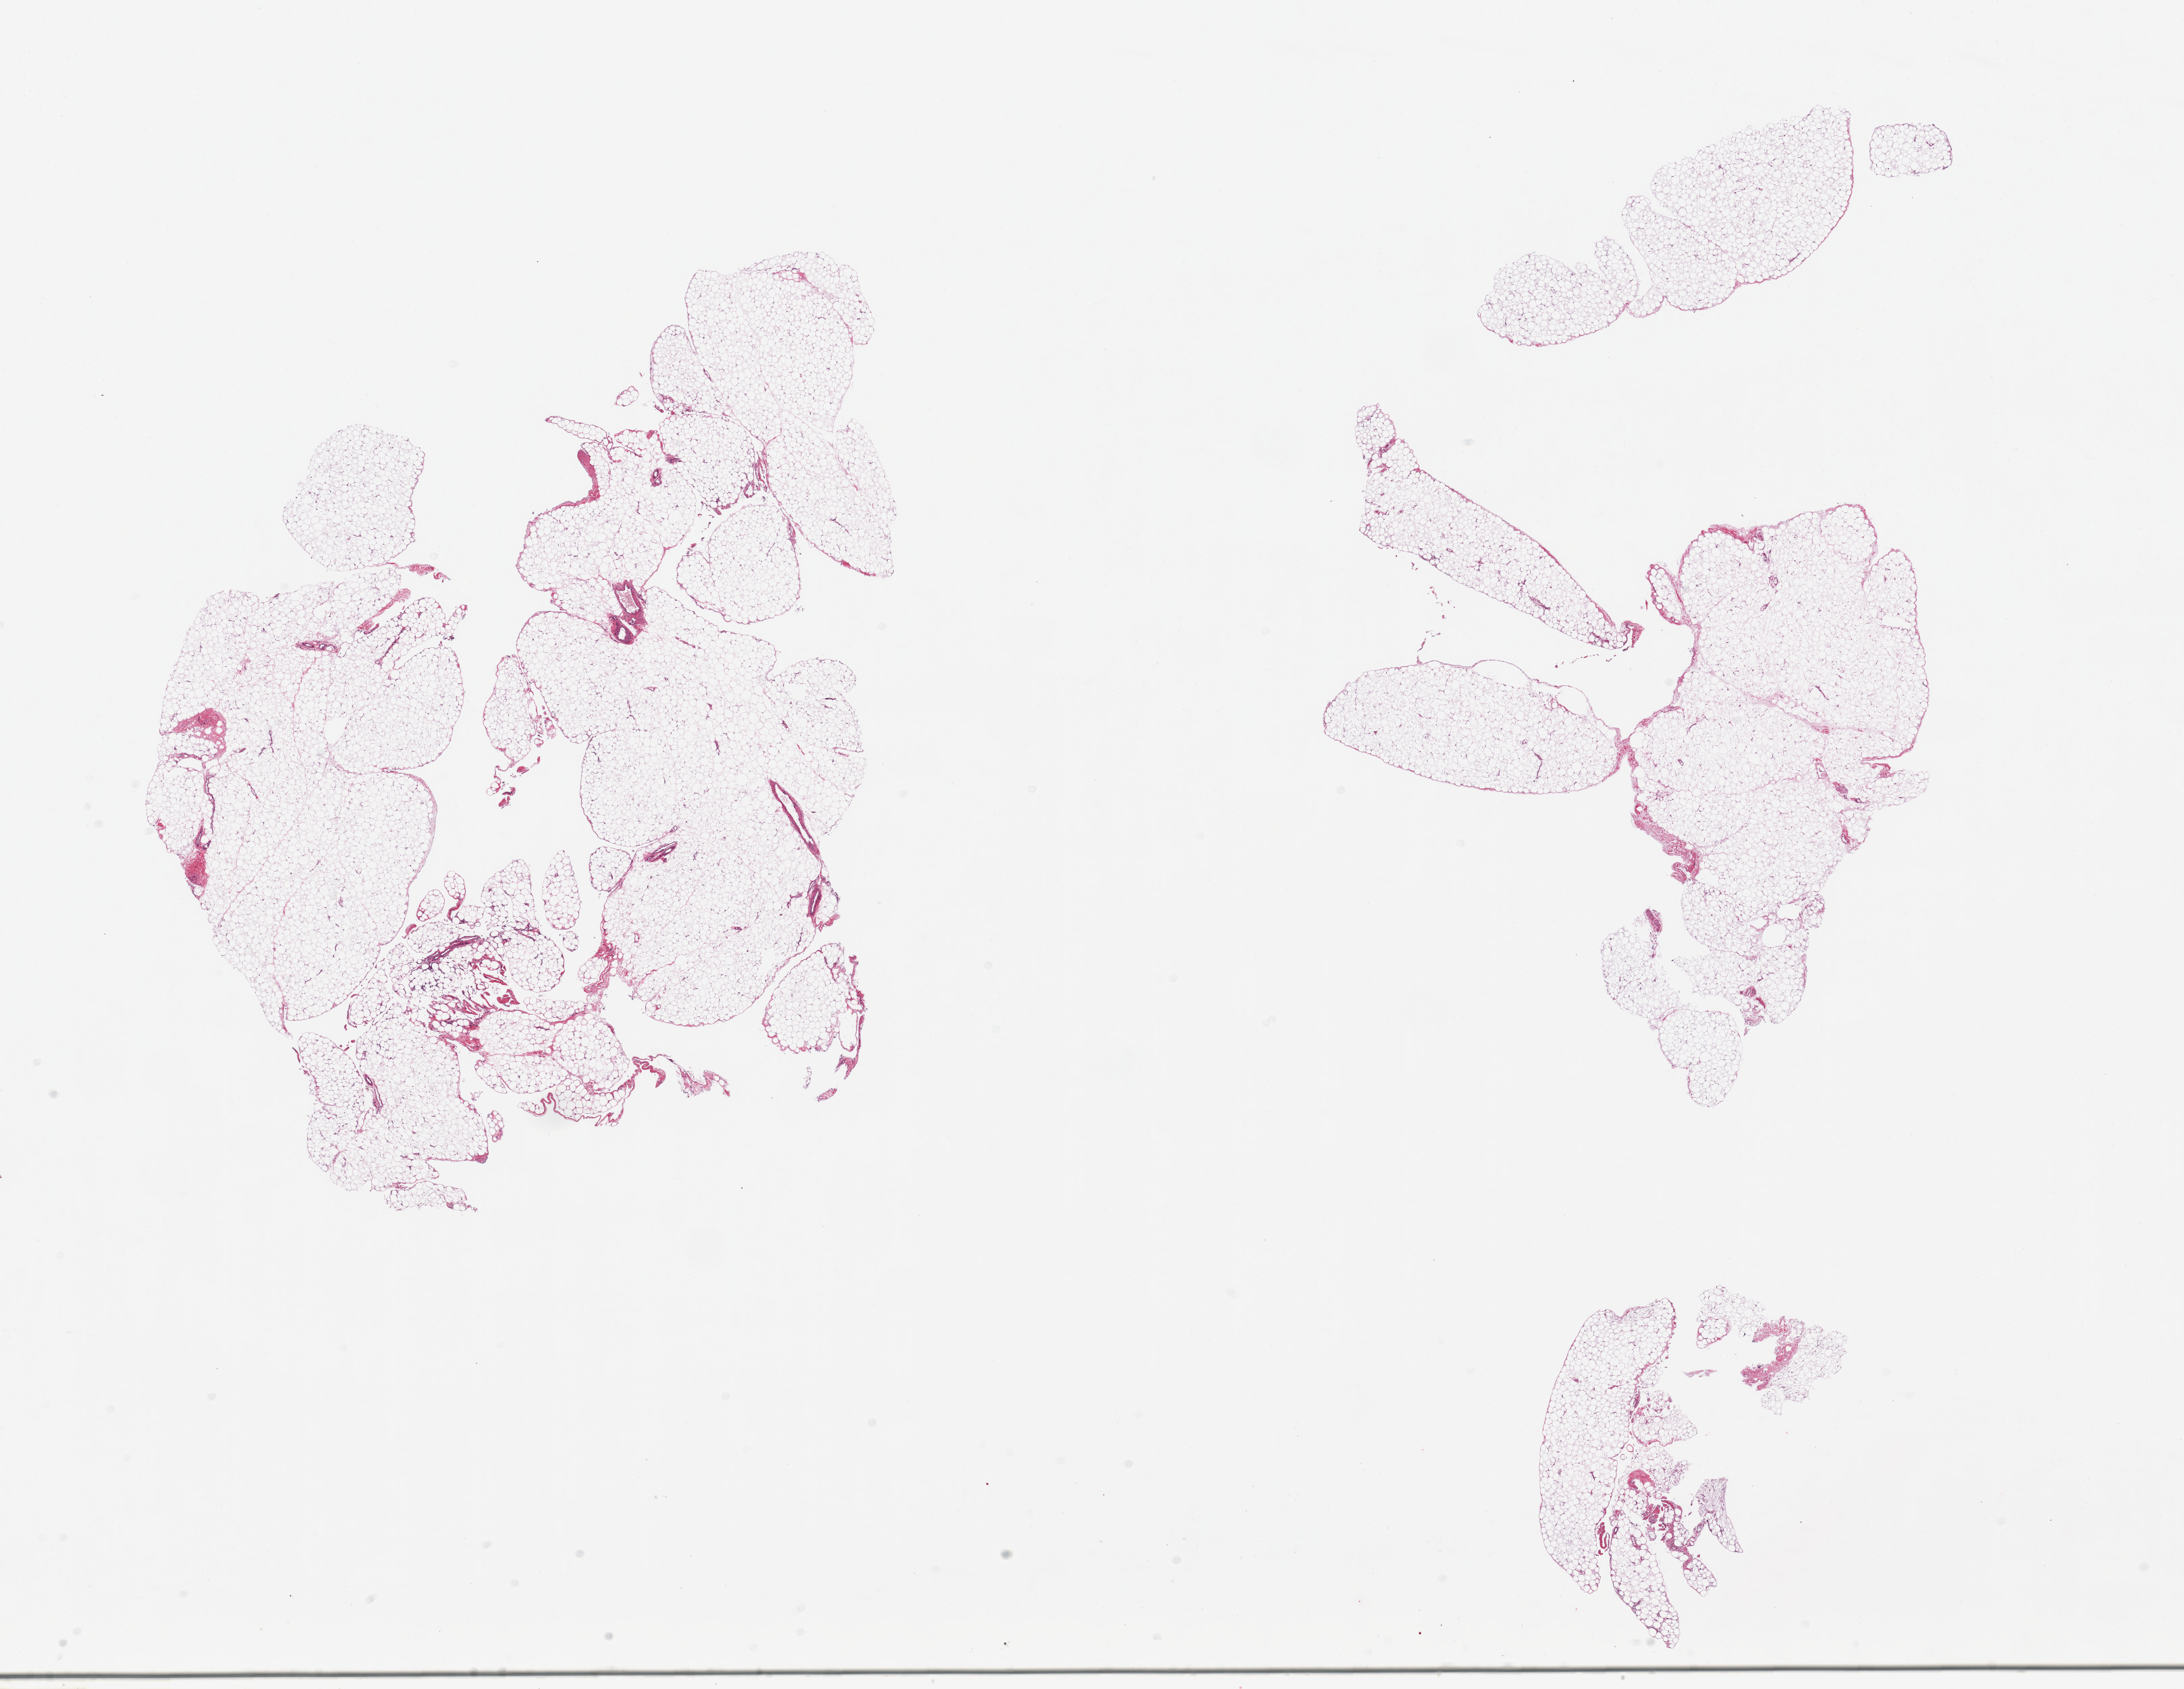
Digitized H&E-stained section, brightfield — shown as a low-resolution overview of the whole scanned area (about 25.6 x 19.8 mm, acquisition: 20x scan), PAXgene-fixed paraffin-embedded (PFPE) section, sampled site (target tissue): omentum, donor tissue sample. Donor: female.
Pathologist's review note for this sample: 2 pieces; lobulated mature adipose tissue with some fibrovascular component.